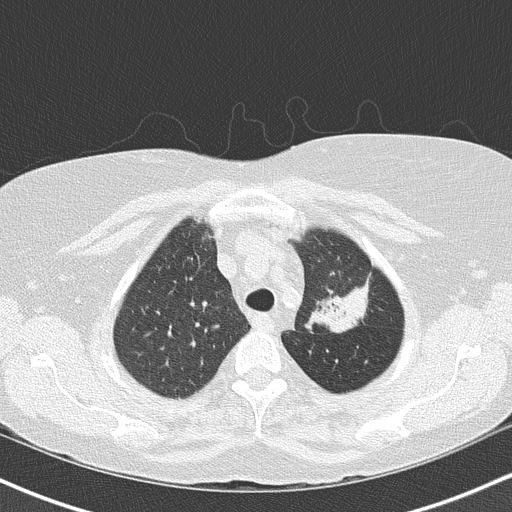
Low-dose screening chest CT, one axial slice; position 122 of 147 along the scan axis; lung window (W 1500 / L -600 HU); 2 mm slice thickness; 512 × 512 image matrix, field of view 320 × 320 mm.
Structures marked on this image (expert manual segmentation):
- lesion 1 (tumor, upper lobe of left lung): bounding box <312,286,368,332> (left, top, right, bottom; pixels)